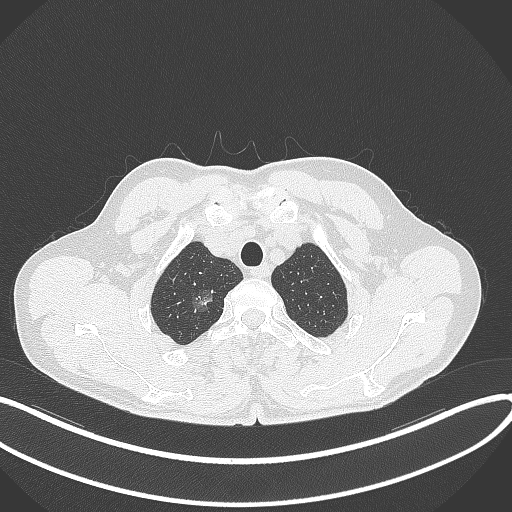
Chest CT, one axial slice. Reconstruction kernel B70f. Lung window (W 1500 / L -600 HU). 512 × 512 image matrix, field of view 400 × 400 mm. Patient: male, 58 years. From the clinical record (not read from this slice): clinical TNM (as recorded): T1c N0 M0; histopathological grade: G1-2.
Annotated regions visible in this slice (bounding box drawn by a radiologist):
- lung tumour (recorded histology: adenocarcinoma): bounding box <187,286,219,315> (left, top, right, bottom; pixels)